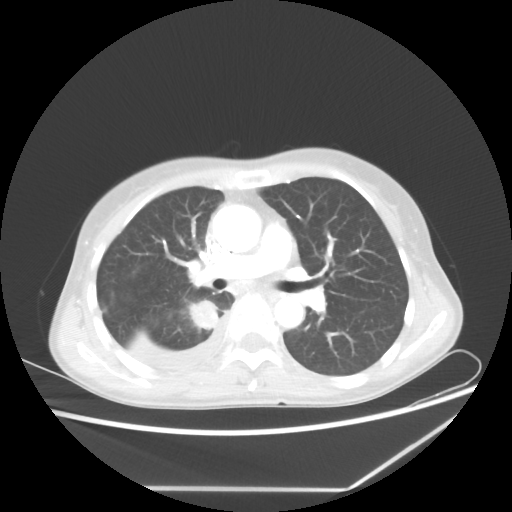
Chest CT, one axial slice; slice 35 of 60 in the series (ordered by position); lung window (W 1500 / L -600 HU); 5 mm slice thickness; 512 × 512 image matrix, field of view 364 × 364 mm. Patient: female, 59 years. From the clinical record (not read from this slice): clinical TNM (as recorded): T1c N1 M1.
Annotated regions visible in this slice (bounding box drawn by a radiologist):
- lung tumour (recorded histology: adenocarcinoma): bounding box [x1, y1, x2, y2] px = [184, 294, 216, 336]